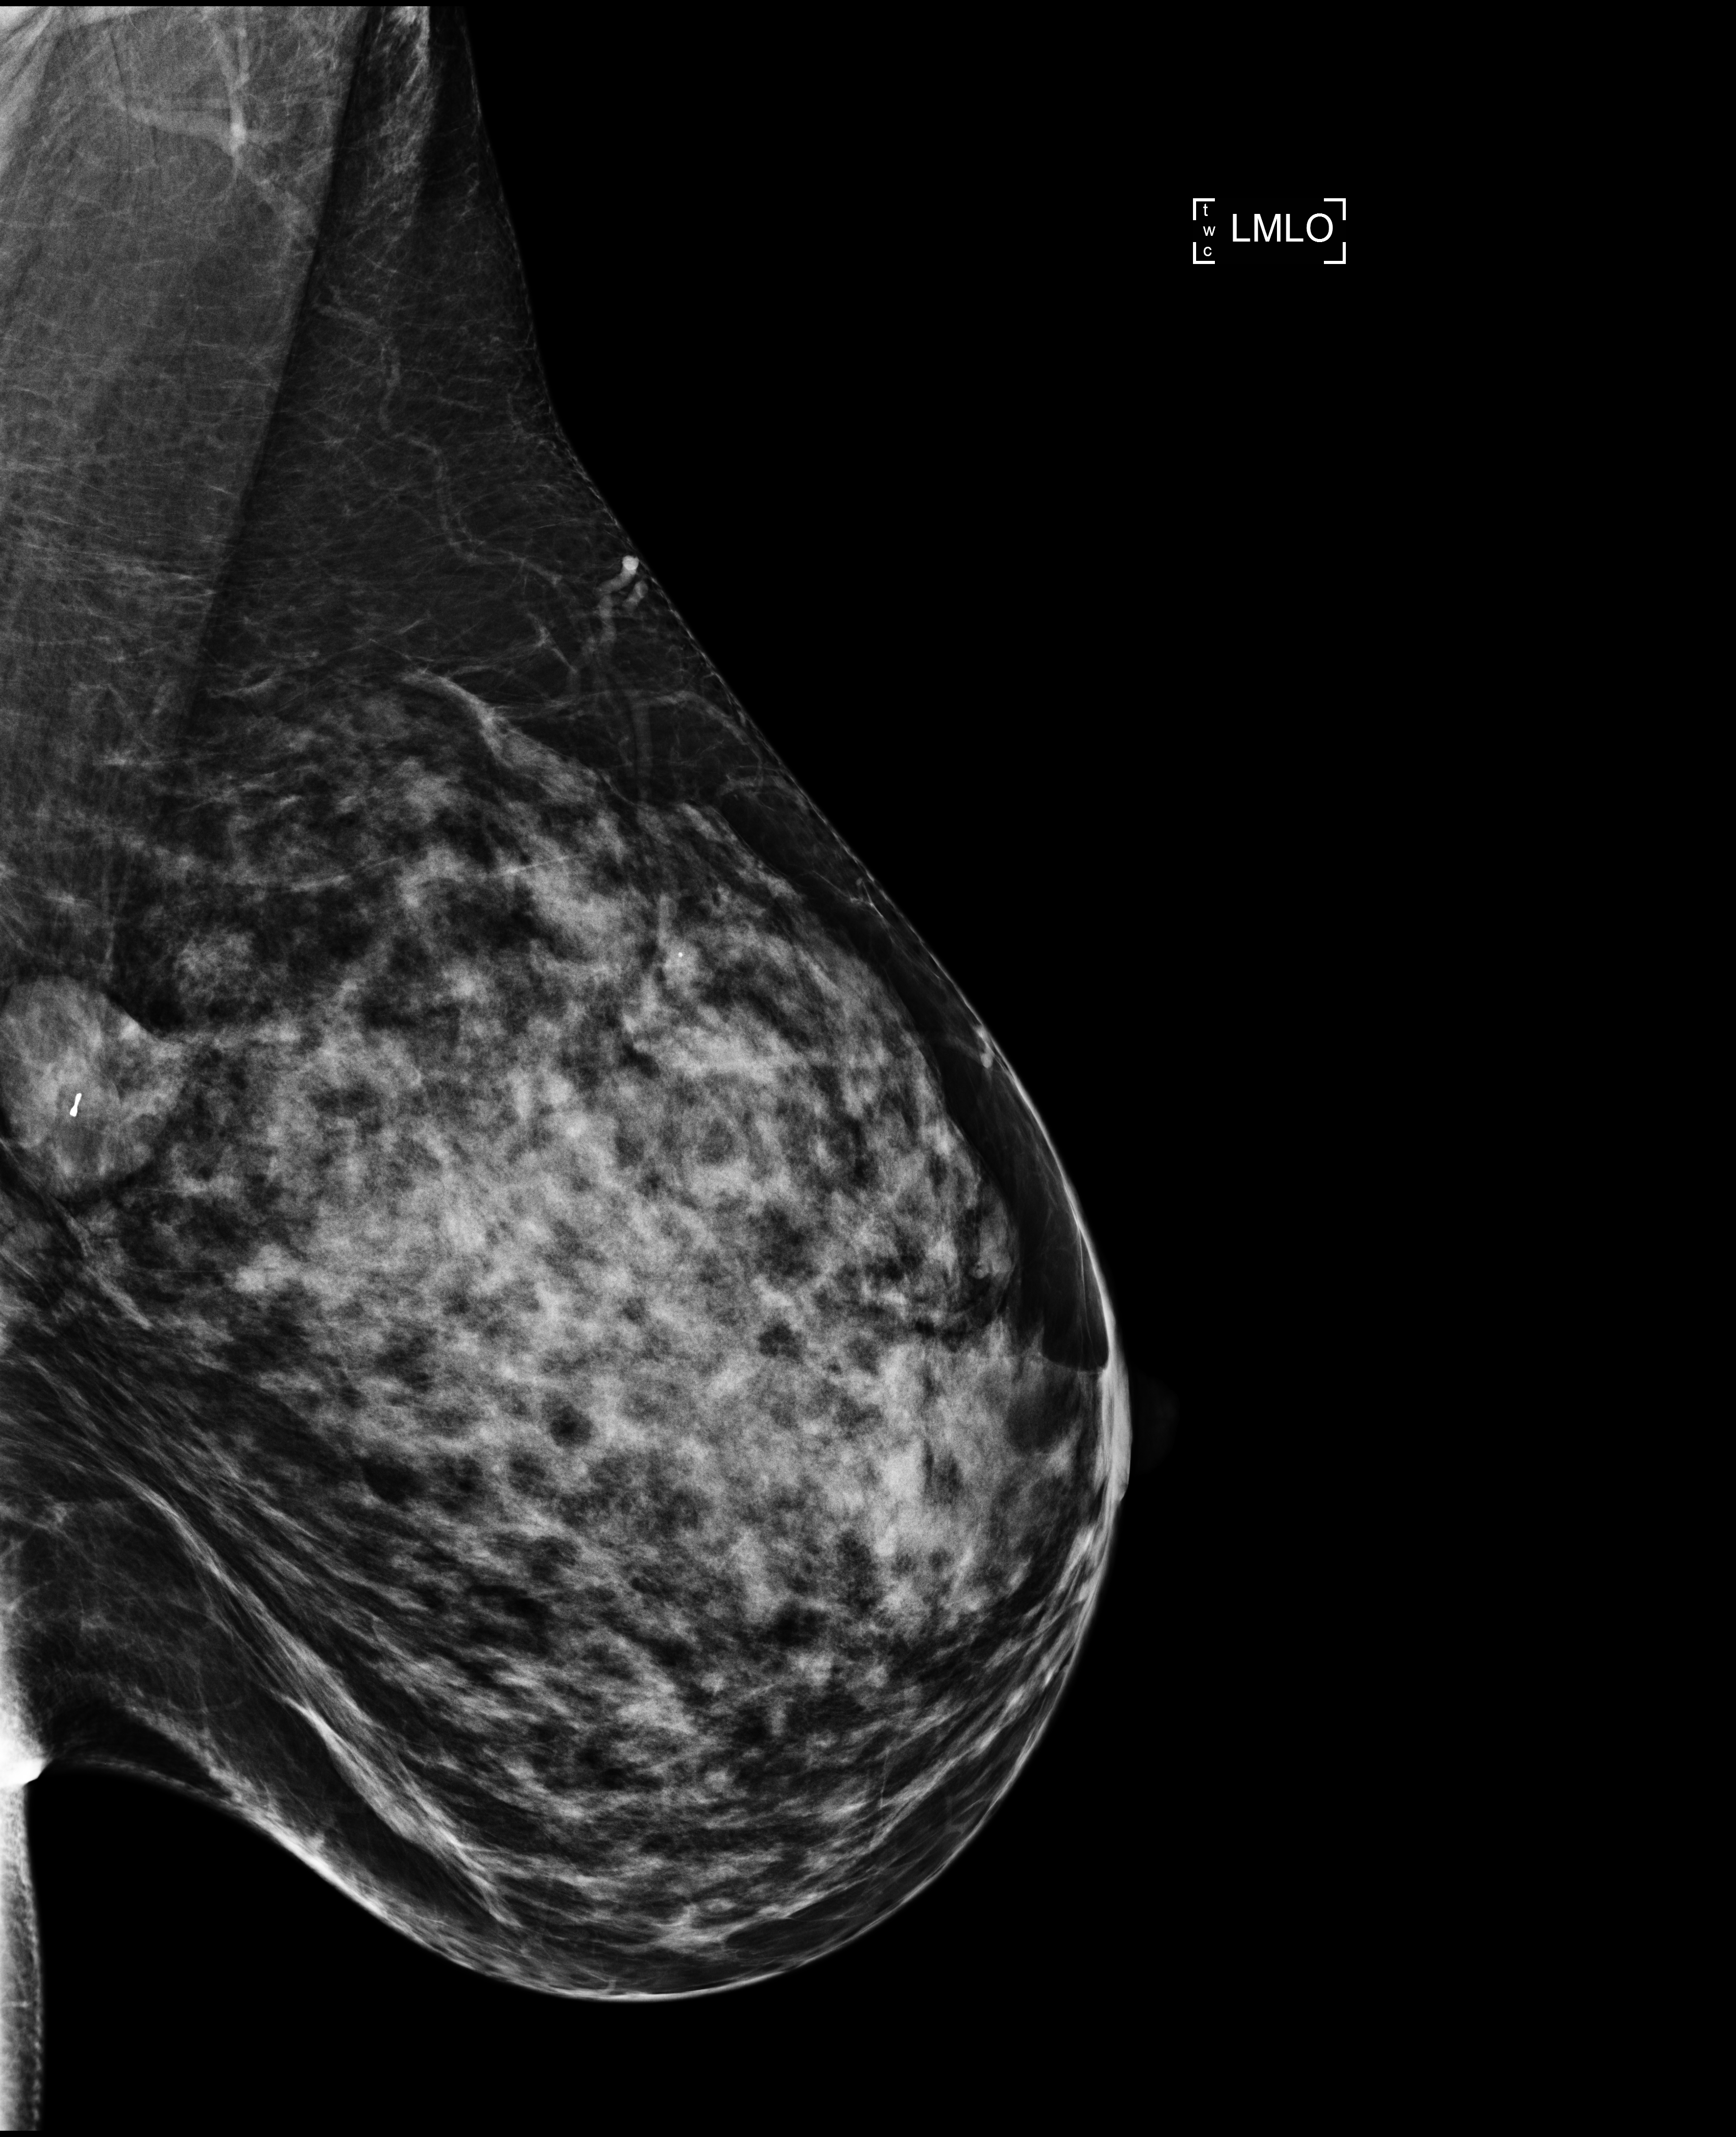
Screening examination. Patient: female, 44 years.
Image type: full-field digital mammogram. Breast: left. Projection: medio-lateral oblique projection.